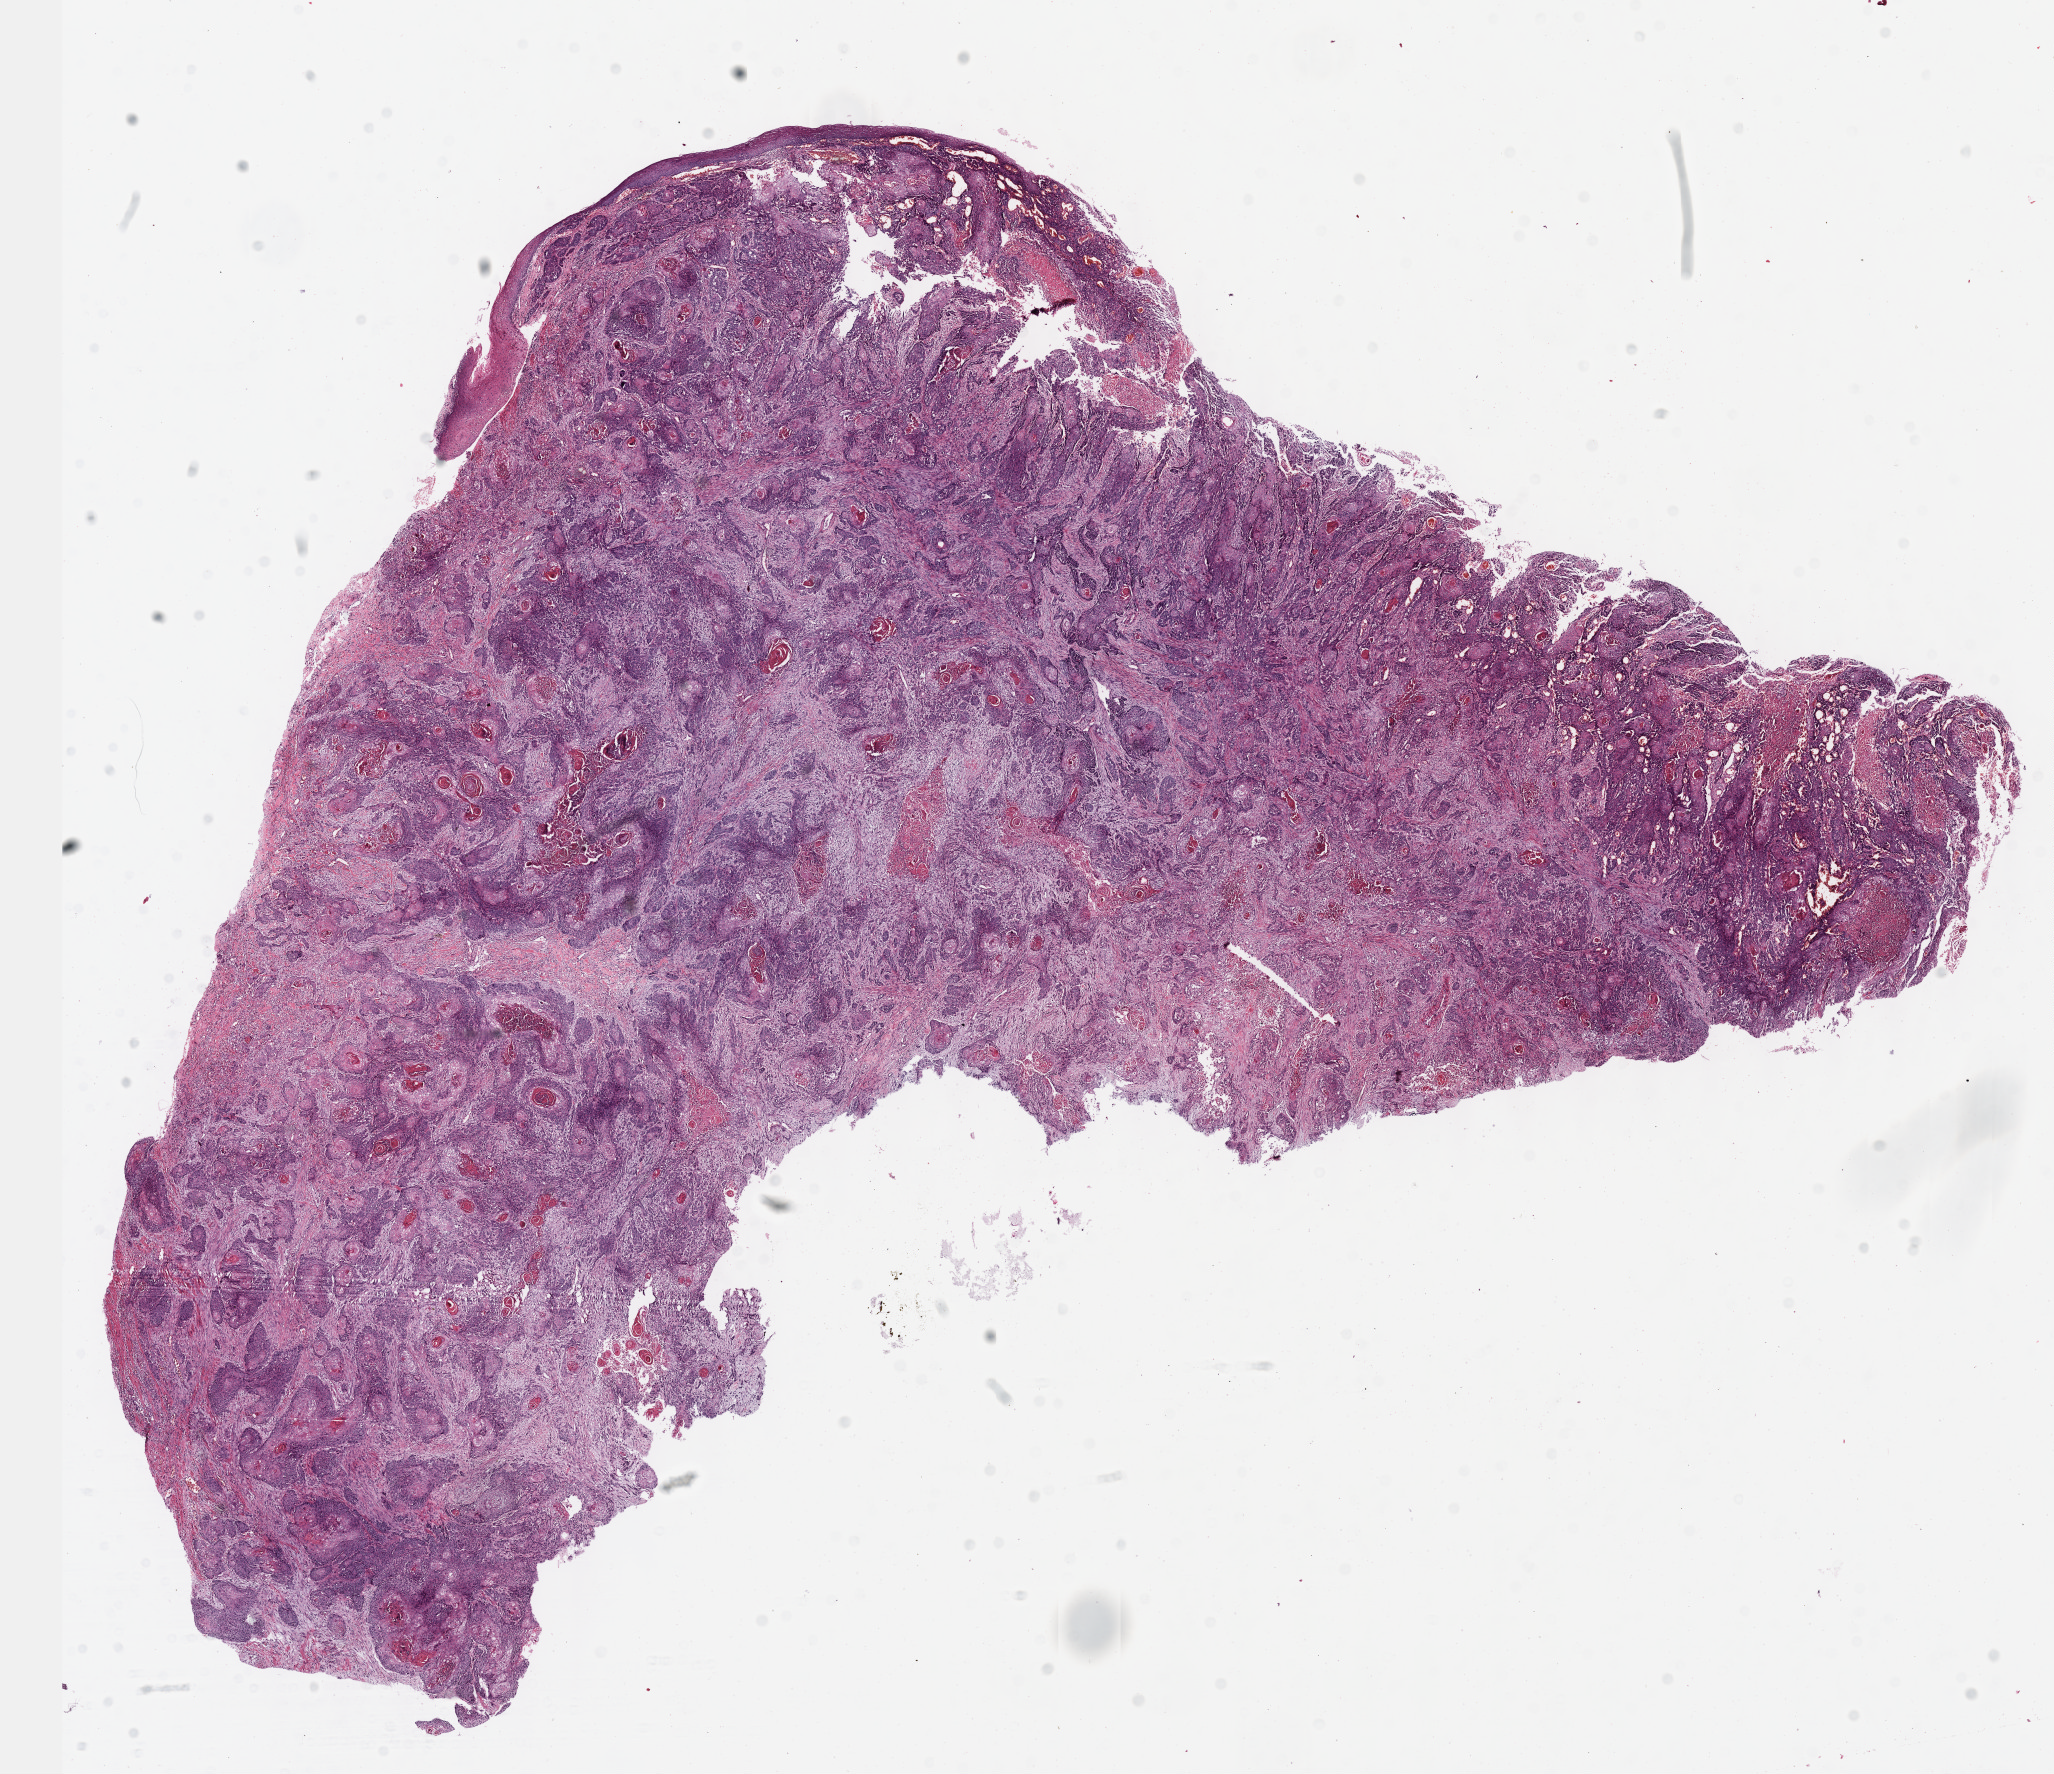
H&E whole-slide image, low-resolution overview of the scanned area, about 16.6 x 14.3 mm (slide scanned at 40x), formalin-fixed paraffin-embedded (FFPE) diagnostic section, primary tumour sample from the esophagus. Male patient; age at initial diagnosis 59 years. Histologic grade: G2 (moderately differentiated).
Diagnosis: Squamous cell carcinoma, NOS (middle third of esophagus). TNM: T2 N0 M0. AJCC pathologic stage: IIA (6th edition).